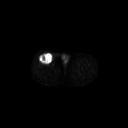
FDG PET of an extremity soft-tissue mass (from a PET/CT study), one axial slice; 3.27 mm slice thickness; 128 × 128 image matrix, field of view 700 × 700 mm. Patient: male, 56 years. From the clinical record (not read from this slice): histological type: pleiomorphic leiomyosarcoma; grade: intermediate; site of the primary tumour: right thigh.
Outlined on this slice (expert contour drawn on MRI and transferred to this co-registered scan by the dataset authors):
- gross tumour volume including surrounding oedema: box from (x=38, y=53) to (x=54, y=64) px
- gross tumour volume (mass): (x=38, y=53)–(x=54, y=64)